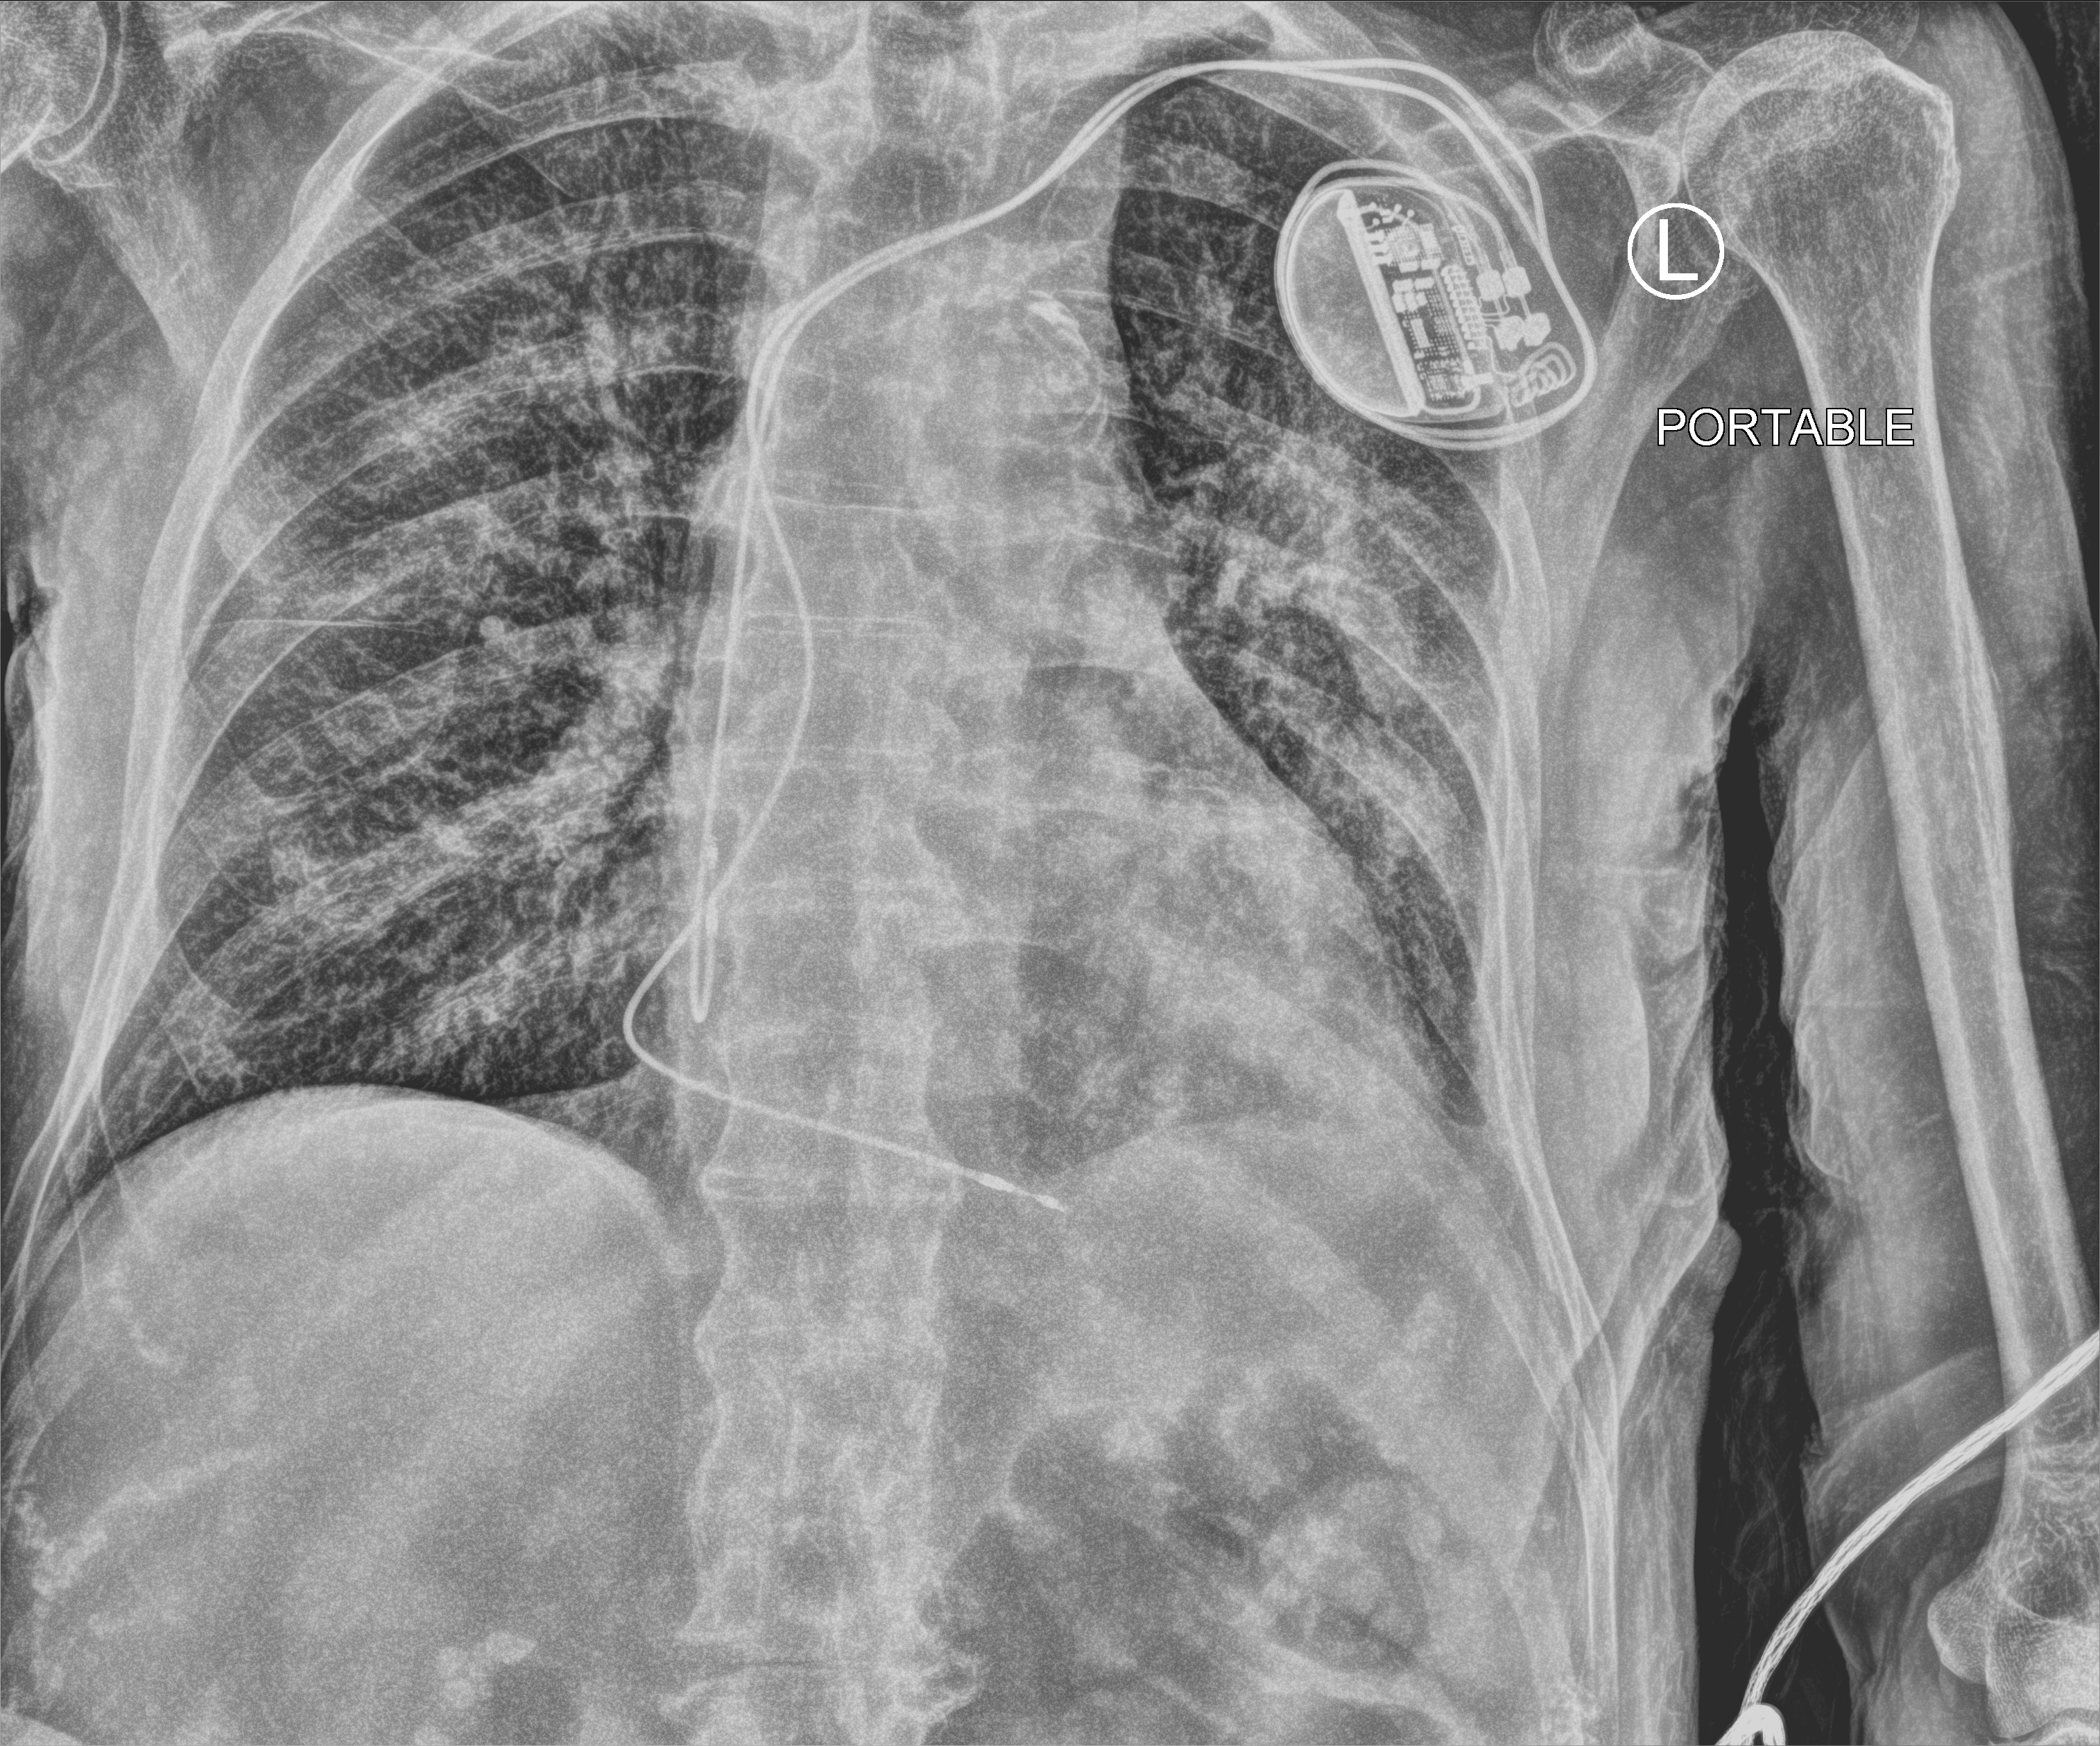
Bedside chest radiograph (computed radiography), anteroposterior (AP) projection. Patient hospitalised with COVID-19; male, aged 75–90 years.
From the hospital-stay record, not from the radiograph (when in the stay this image was taken is not recorded): admitted to intensive care during this hospital stay: no.